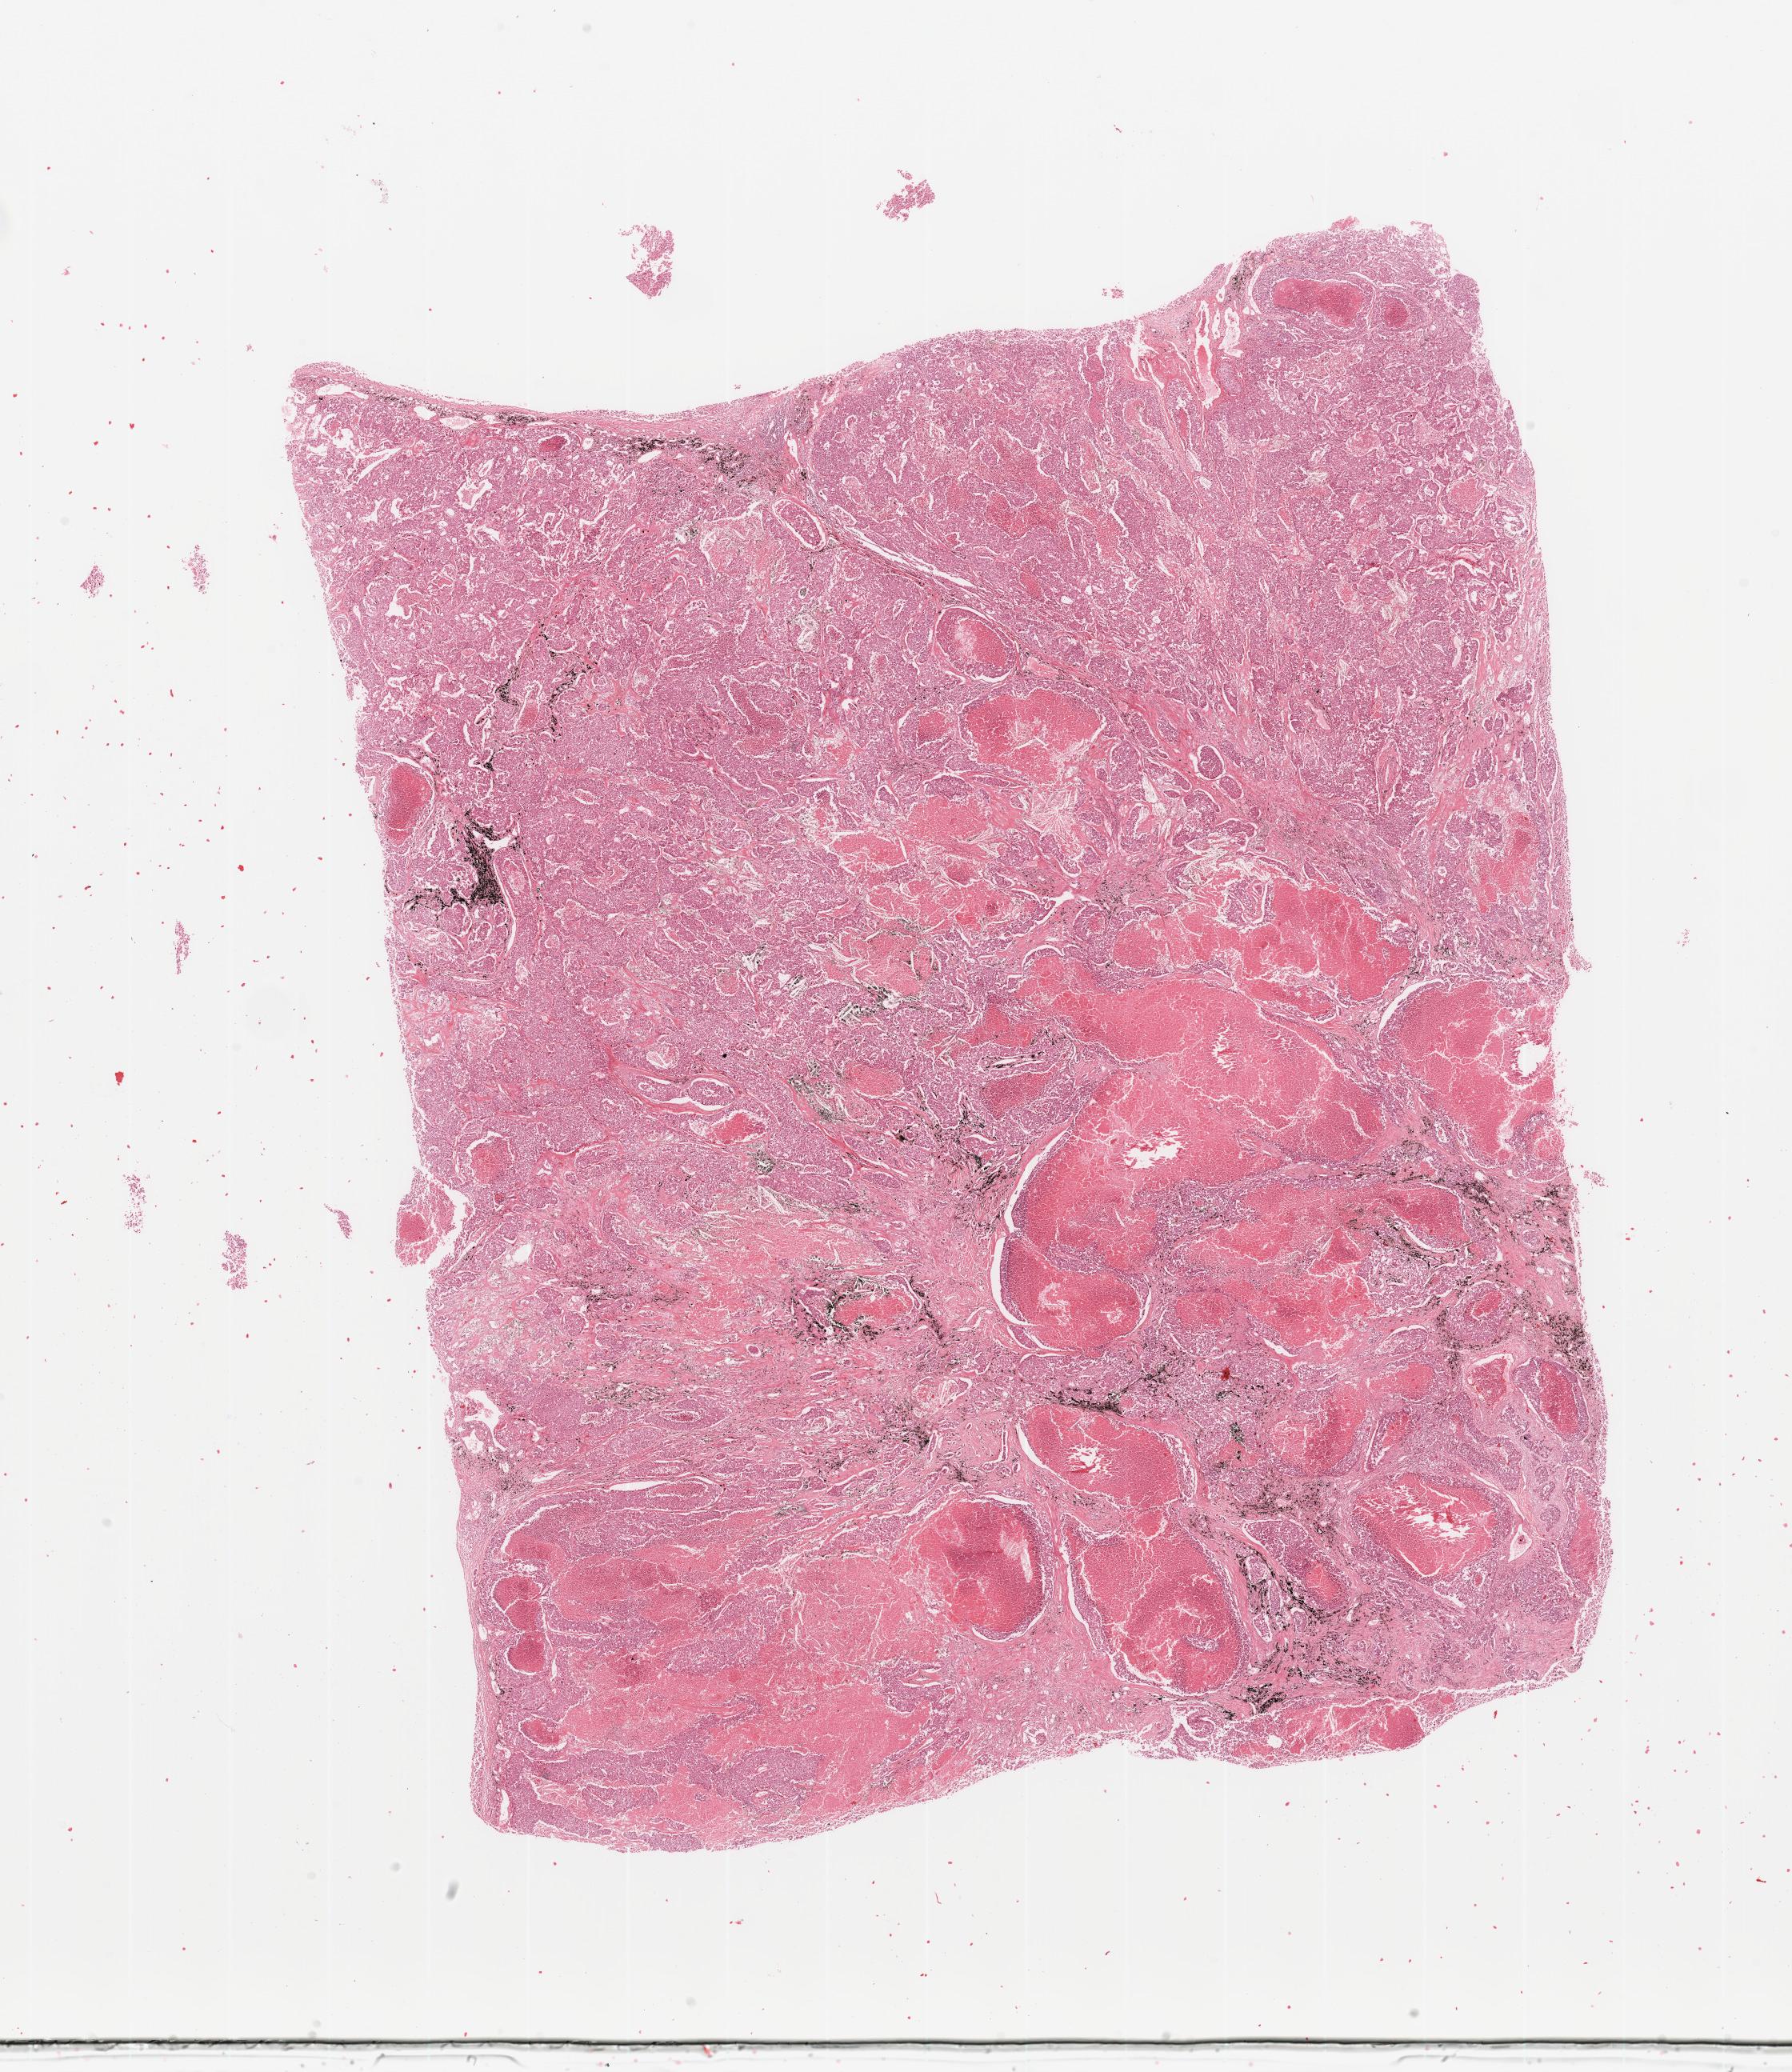
Digitized Hematoxylin and eosin (H&E) stained tissue section (whole slide), low-resolution overview of the scanned area, about 17.7 x 20.5 mm (acquisition: 20x scan). Tumour tissue sample, sampled site: lung. Male, 56 y/o. Histologic grade: G3 (poorly differentiated). Pathologist review of this section (percent, as recorded): tumour nuclei 80%, necrosis 20%.
Histologic diagnosis: Adenocarcinoma, NOS. AJCC pathologic stage: IIIA.